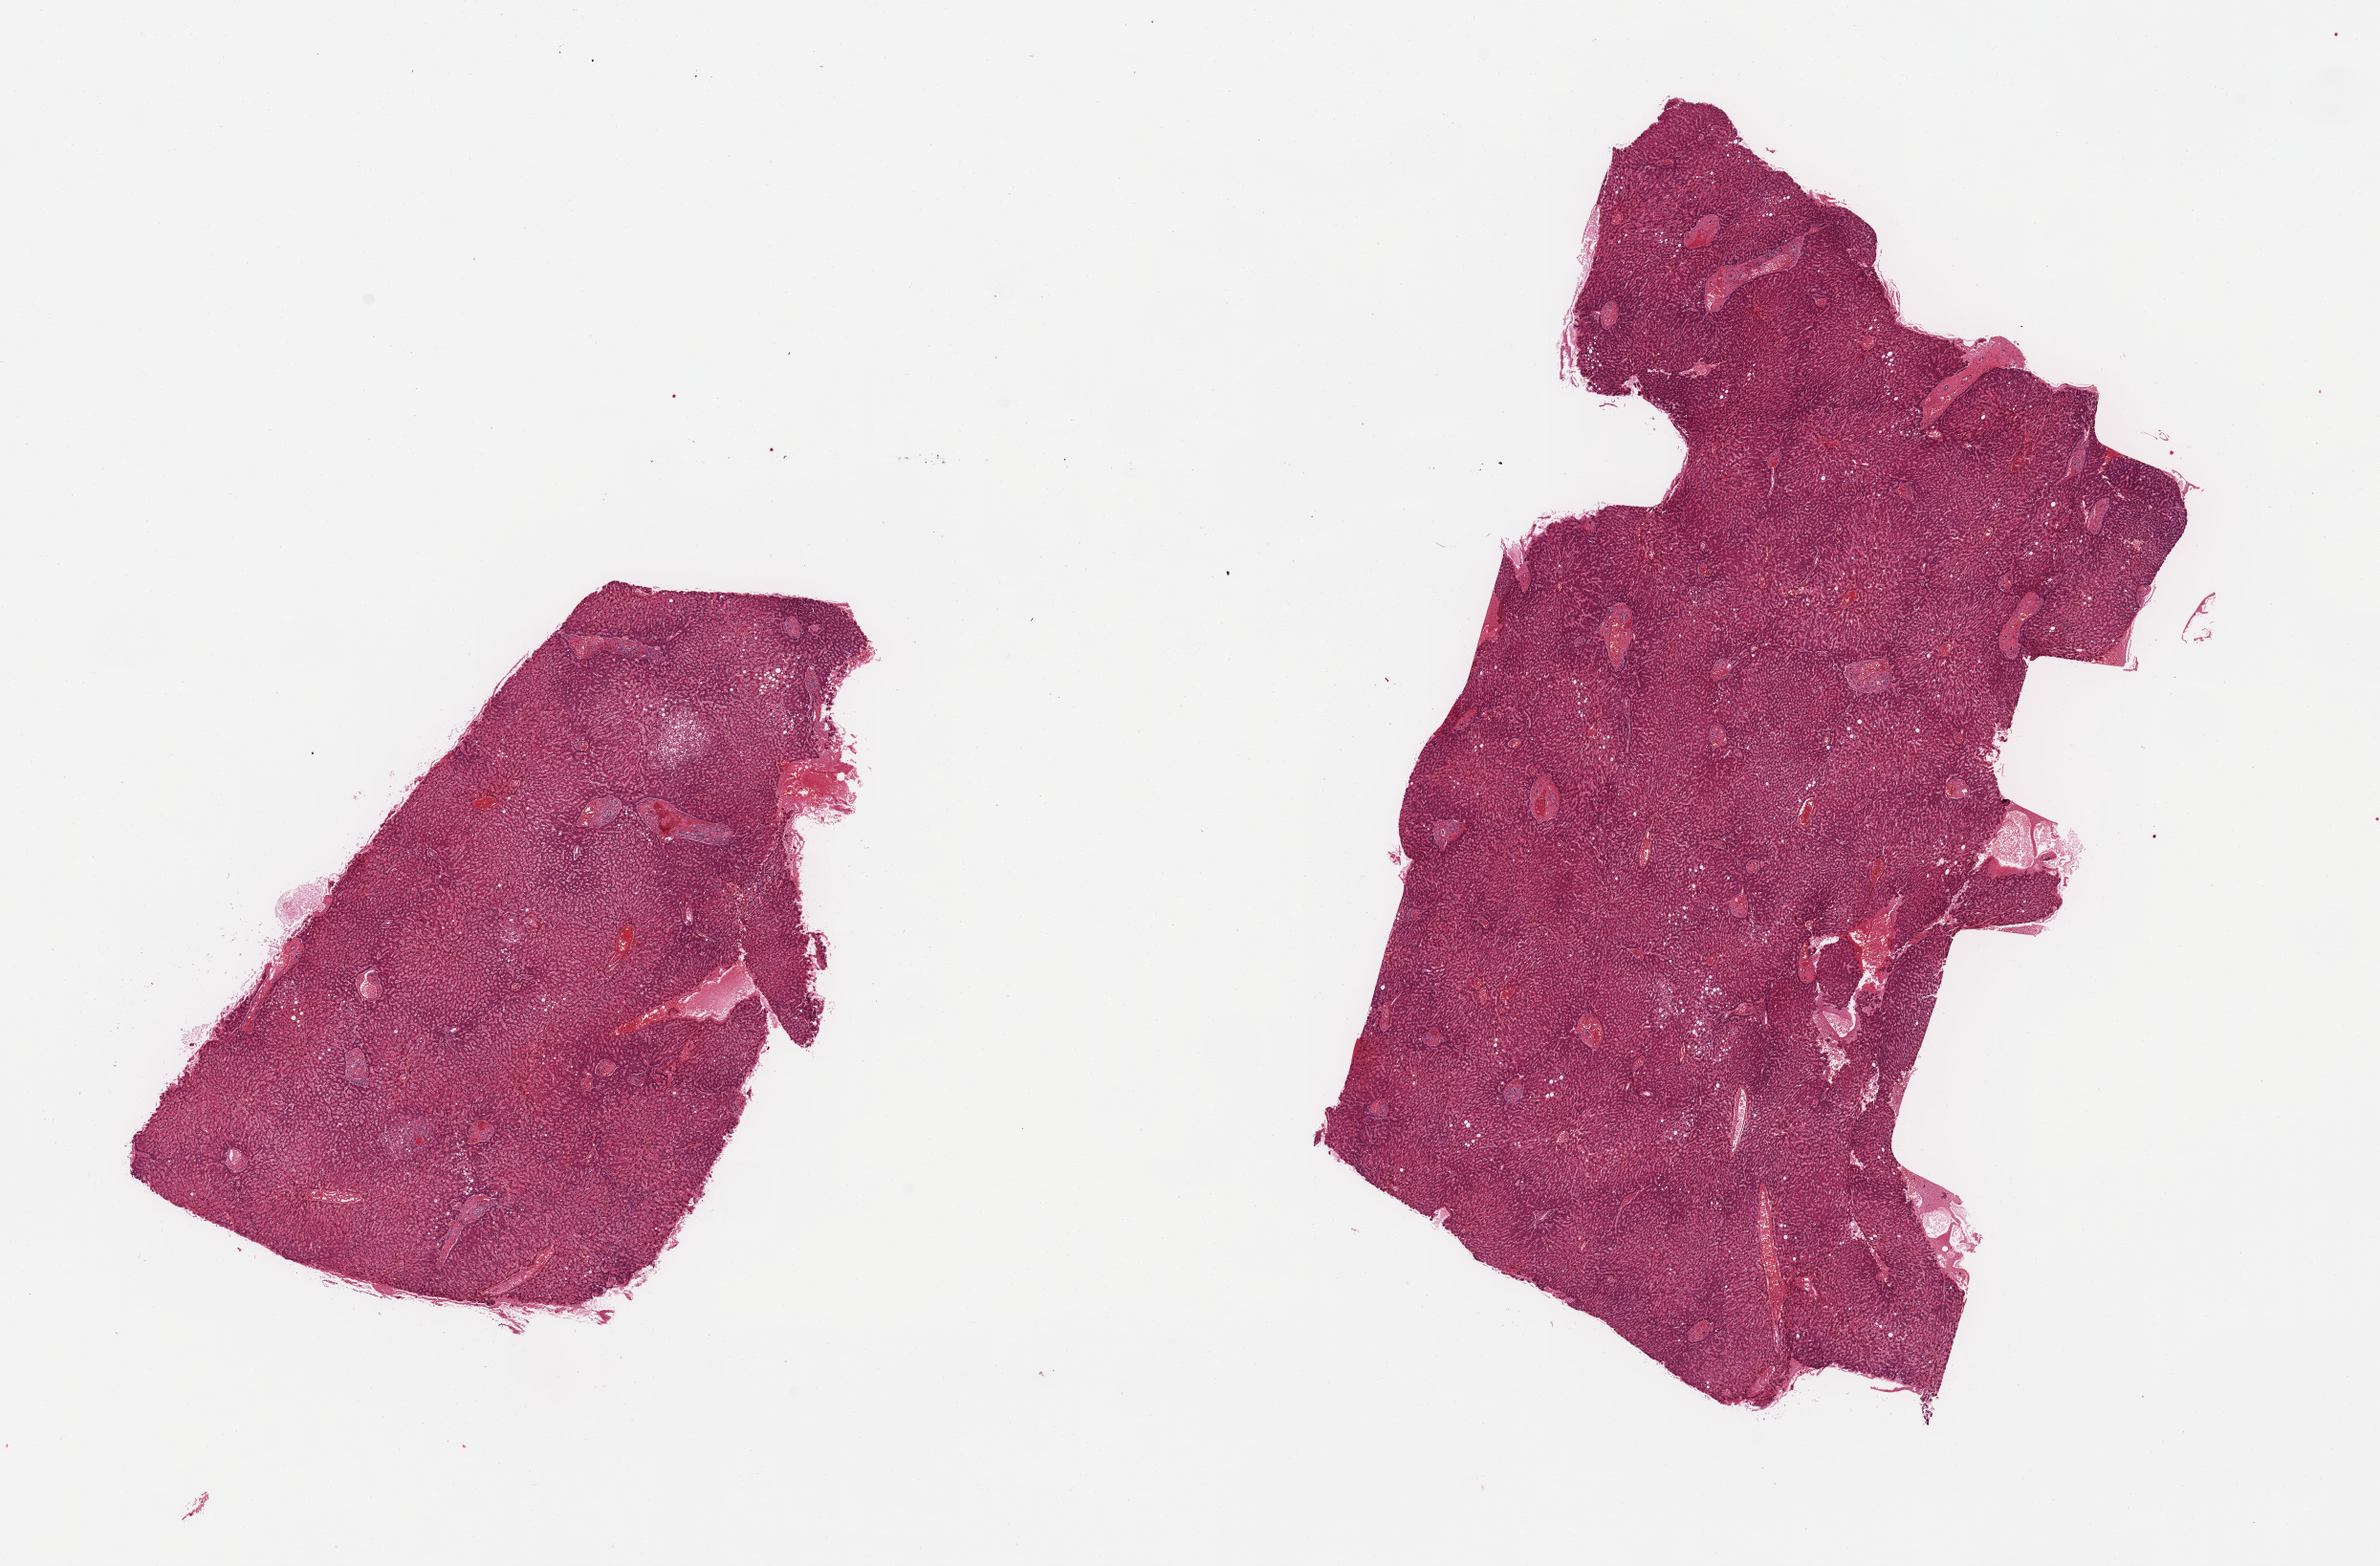
Whole-slide image, hematoxylin and eosin (H&E) stain, shown as a low-resolution overview of the whole scanned area (about 19.7 x 13.0 mm); PAXgene-fixed, paraffin-embedded tissue; sampled site (target tissue): liver; tissue donor sample. Donor: male.
Reviewer comment on this tissue sample: 2 pieces; 5% macrosteatosis.